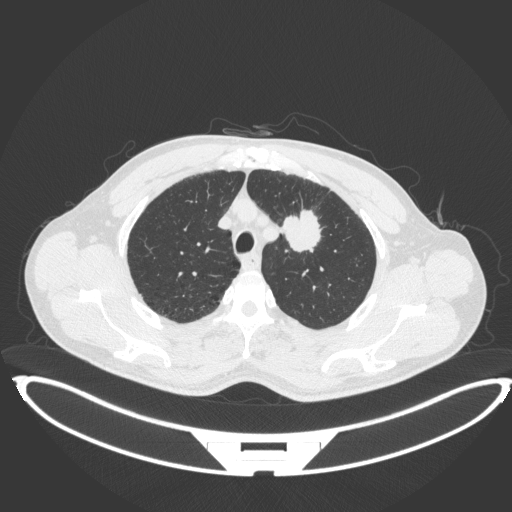
Chest CT, one axial slice. Slice 350 of 407 in the series (ordered by position). 120 kVp. Lung window (W 1500 / L -600 HU). 512 × 512 image matrix. Male patient, age 60 years. From the clinical record (not read from this slice): clinical TNM (as recorded): T2a N0 M0.
Annotated regions visible in this slice (rectangle marked by the reading radiologist):
- lung tumour (recorded histology: squamous cell carcinoma): bounding box [x1, y1, x2, y2] px = [276, 208, 324, 255]